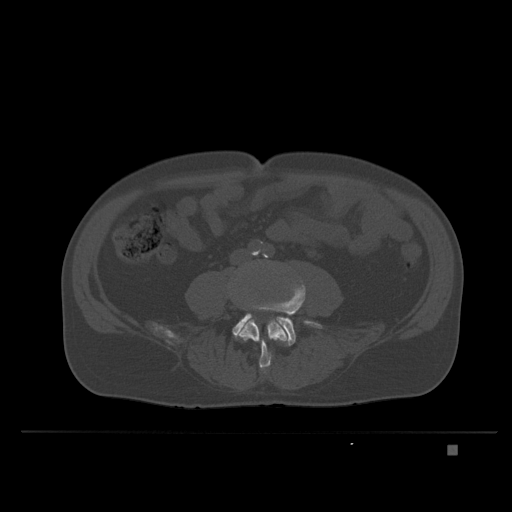
CT including the spine, one axial slice. Position 67 of 435 along the scan axis. Bone window (W 1800 / L 400 HU). 1.5 mm slice thickness. 512 × 512 image matrix, field of view 434 × 434 mm. Male patient, age 73 years. Case-level facts recorded for this patient, not image findings: primary cancer: skin.
Structures marked on this image (semi-automatically segmented with operator editing):
- L4 vertebra: bounding box [x1, y1, x2, y2] px = [229, 292, 288, 373]
- L5 vertebra: [233, 286, 322, 346]